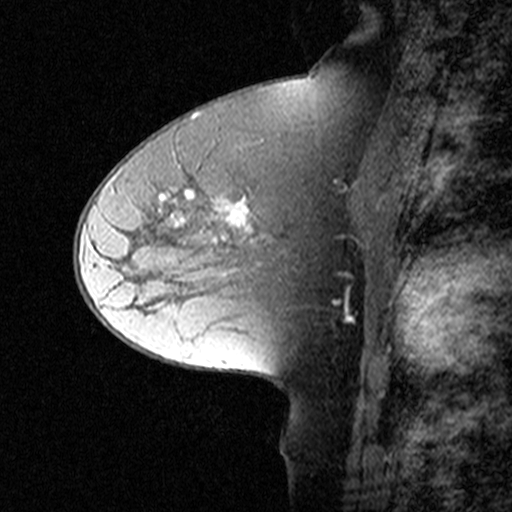
Breast MRI (dynamic contrast-enhanced), one sagittal slice. Position 26 of 44 along the scan axis. Dynamic contrast-enhanced study with each time point stored as its own series, time point 2 of 3 at this slice position (early post-contrast, ordered by acquisition time). 1.5 T. TE 4.5 ms, TR 11 ms. 3 mm slice thickness. 512 × 512 image matrix, field of view 200 × 200 mm. Patient: female, 50 years. Case-level facts recorded for this patient, not image findings: setting: breast cancer imaged before/during neoadjuvant chemotherapy; receptor status: HR-positive, HER2-negative.
Annotated regions visible in this slice (semi-automatic segmentation, software-assisted and operator-edited):
- analysis volume of interest (the breast-tissue region the enhancement analysis was run in; not a lesion): bounding box [x1, y1, x2, y2] px = [126, 162, 329, 291]
- tumour enhancement mask (voxels above the 90 % enhancement threshold inside the analysis volume of interest): [160, 194, 253, 233]